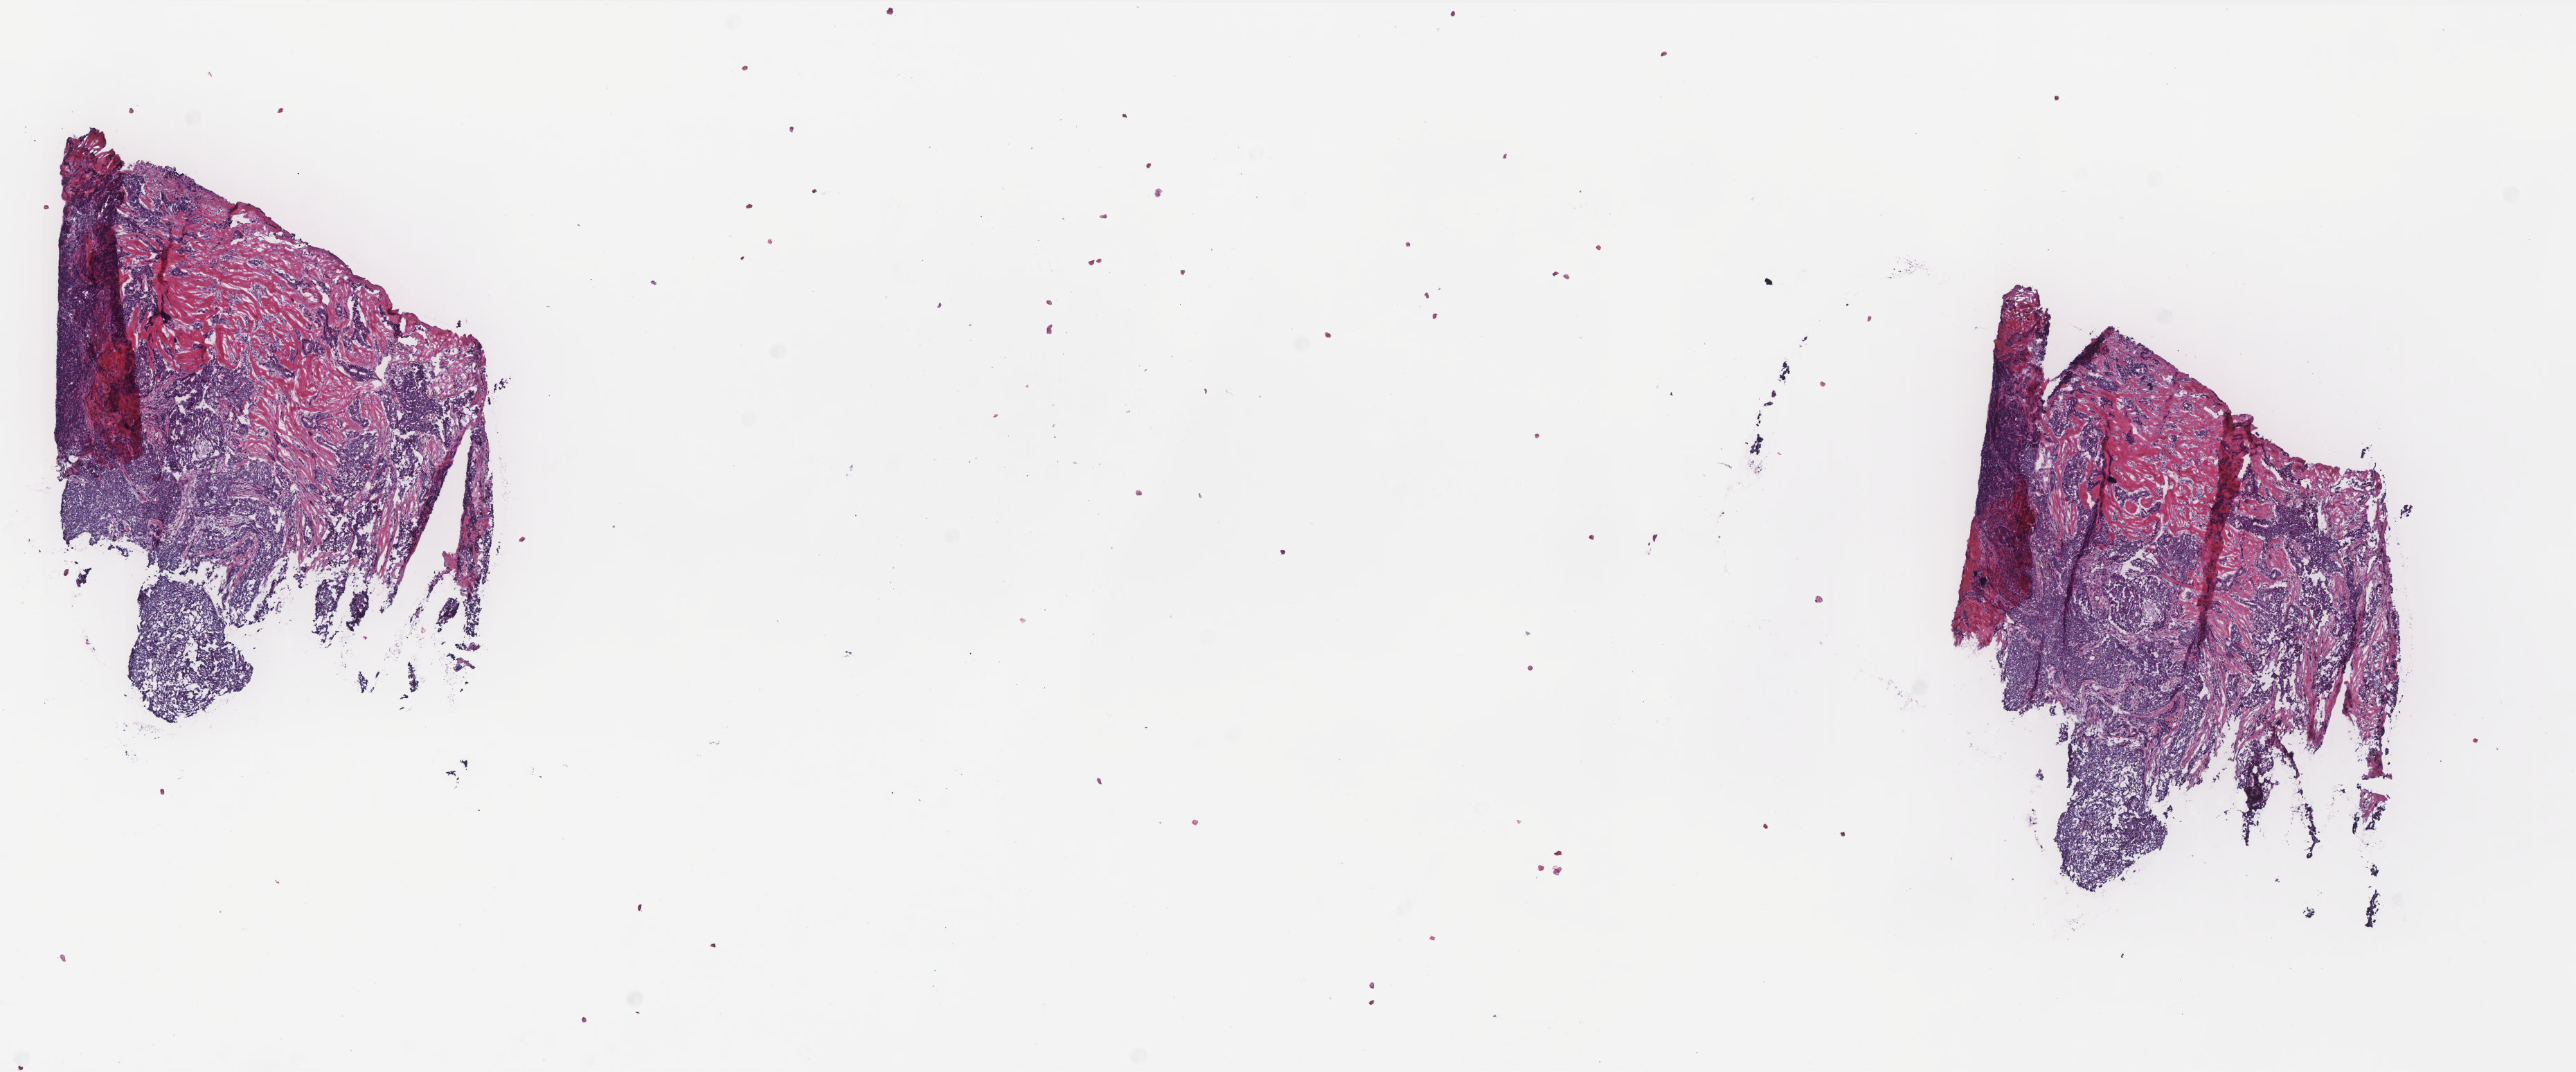
Whole-slide histology image, Hematoxylin and eosin (H&E) stained, low-resolution overview of the scanned area, about 14.9 x 6.2 mm. Frozen section. Breast, primary tumour sample. Female, age 84 years at initial diagnosis. Pathologist review of this section (percent, as recorded): tumour cells 60%, tumour nuclei 60%, normal cells 0%, stromal cells 30%, necrosis 10%. Inflammatory infiltration, as recorded: lymphocyte infiltration 40%, monocyte infiltration 20%, neutrophil infiltration 20%.
AJCC pathologic stage: IIIA (7th edition). Laterality: right. Histologic diagnosis: Infiltrating duct carcinoma, NOS. Lymph nodes positive (case pathology): 13 of 19 examined.